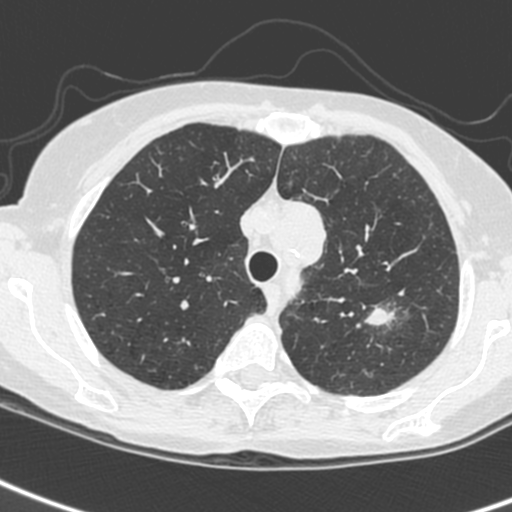
Low-dose screening chest CT, one axial slice. Slice 194 of 242 in the series (ordered by position). 120 kVp. Lung window (W 1500 / L -600 HU). 1.3 mm slice thickness. 512 × 512 image matrix.
Outlined on this slice (outlined manually by an expert reader):
- lesion 1 (tumor, upper lobe of left lung): bounding box [x1, y1, x2, y2] px = [367, 307, 388, 327]
- lesion 3 (tumor, upper lobe of left lung): [292, 200, 327, 266]